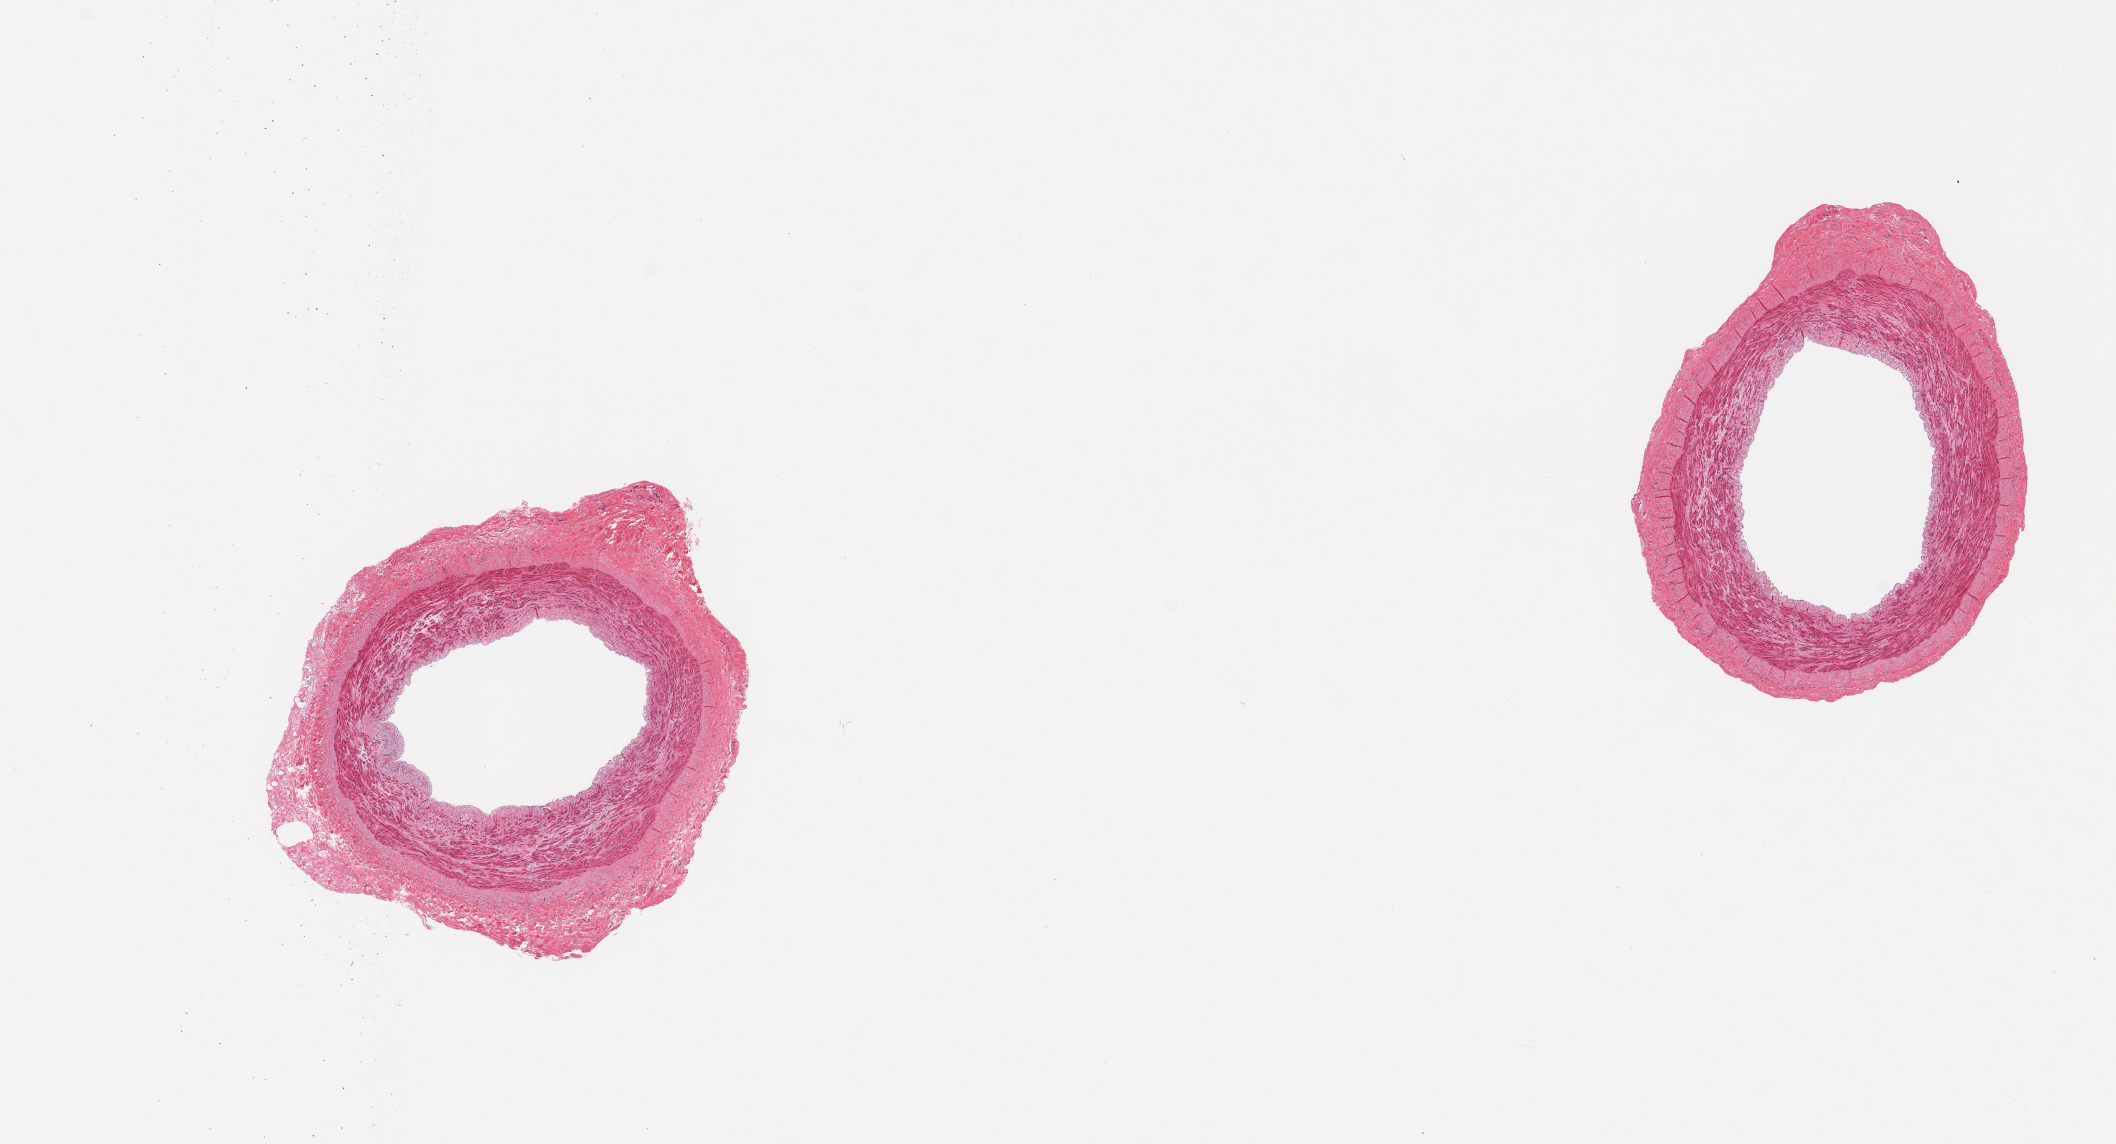
Digitized H&E-stained section — whole scanned area (about 16.7 x 9.0 mm) shown as a low-resolution overview, PAXgene-fixed, paraffin-embedded tissue, sampled site (target tissue): tibial artery, donor tissue sample.
Pathologist's review note for this sample: 2 pieces; no plaques; well trimmed.